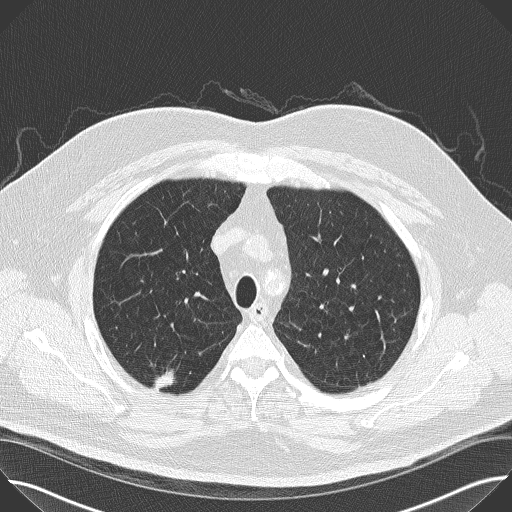
Low-dose screening chest CT, one axial slice; lung window (W 1500 / L -600 HU); 2 mm slice thickness; 512 × 512 image matrix.
Structures marked on this image (manually delineated by an expert):
- lesion 1 (tumor, upper lobe of right lung): bounding box (x1, y1, x2, y2) in pixels: (153, 369, 175, 393)